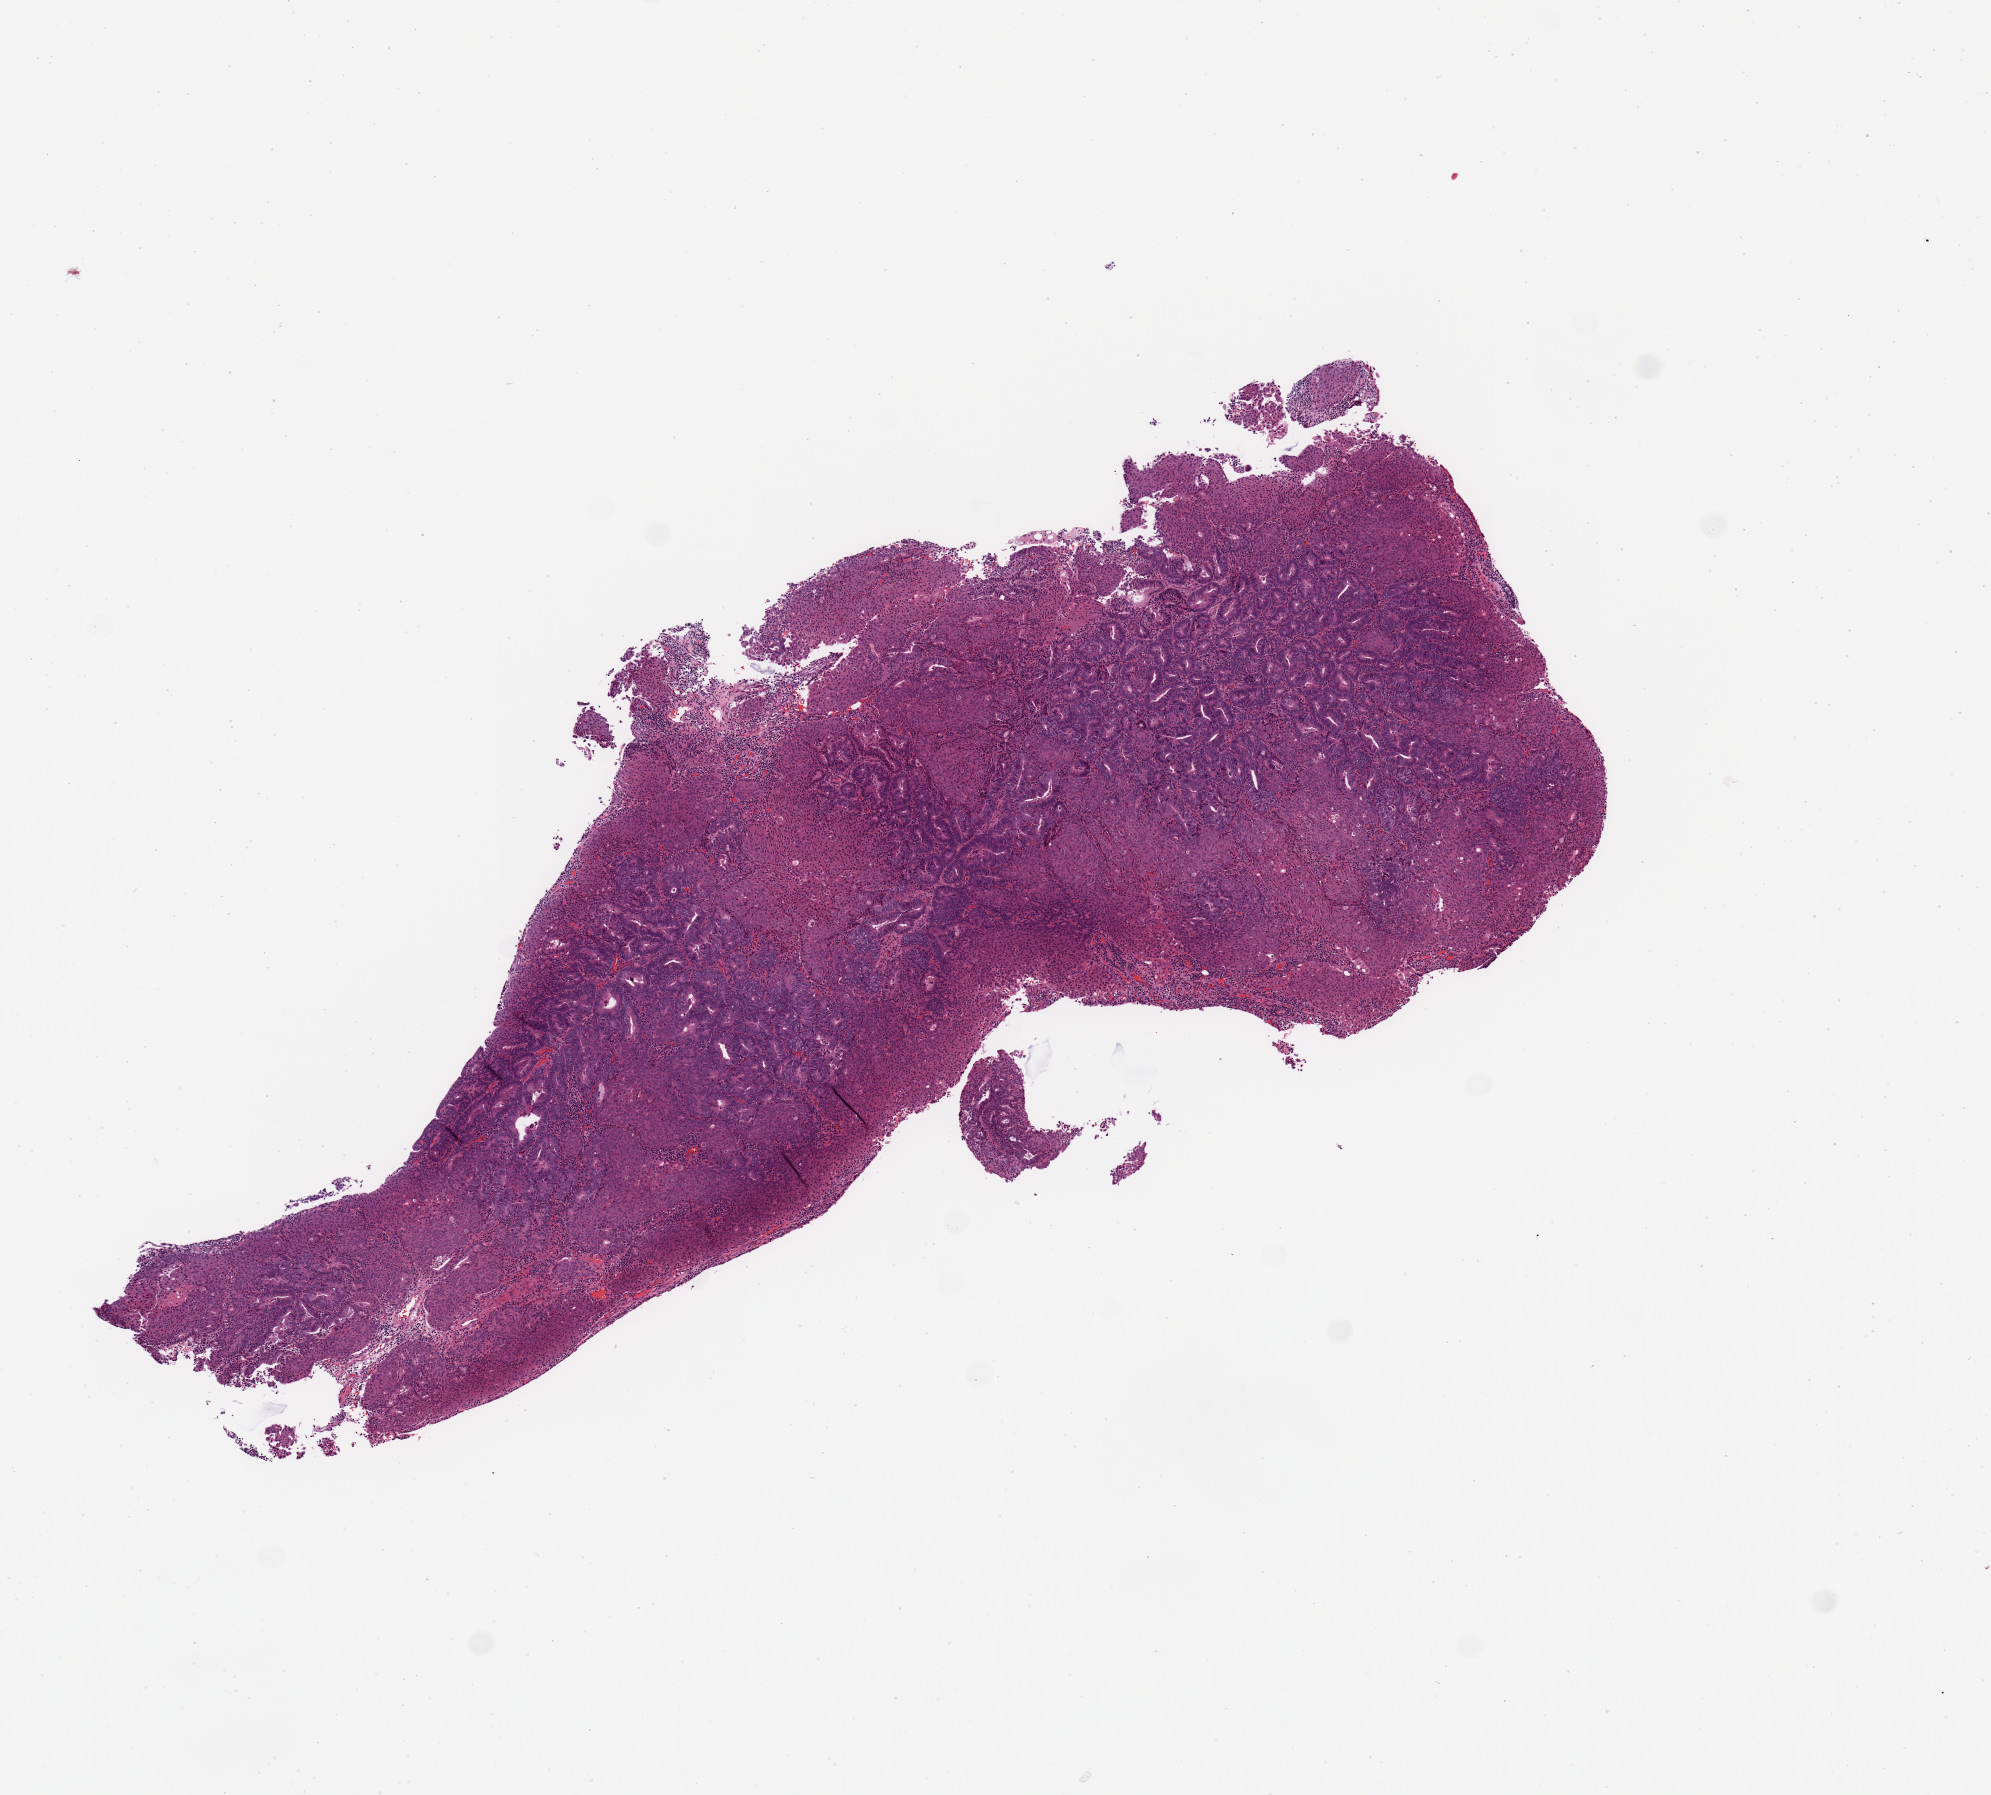
Digitized H&E-stained tissue section (whole slide) — shown as a low-resolution overview of the whole scanned area (about 7.9 x 7.1 mm, acquisition: 20x scan), uterus, tumour tissue. Patient: female, age 50 years. Histologic grade: G1 (well differentiated).
Diagnosis: Endometrioid adenocarcinoma, NOS. AJCC pathologic stage: I.